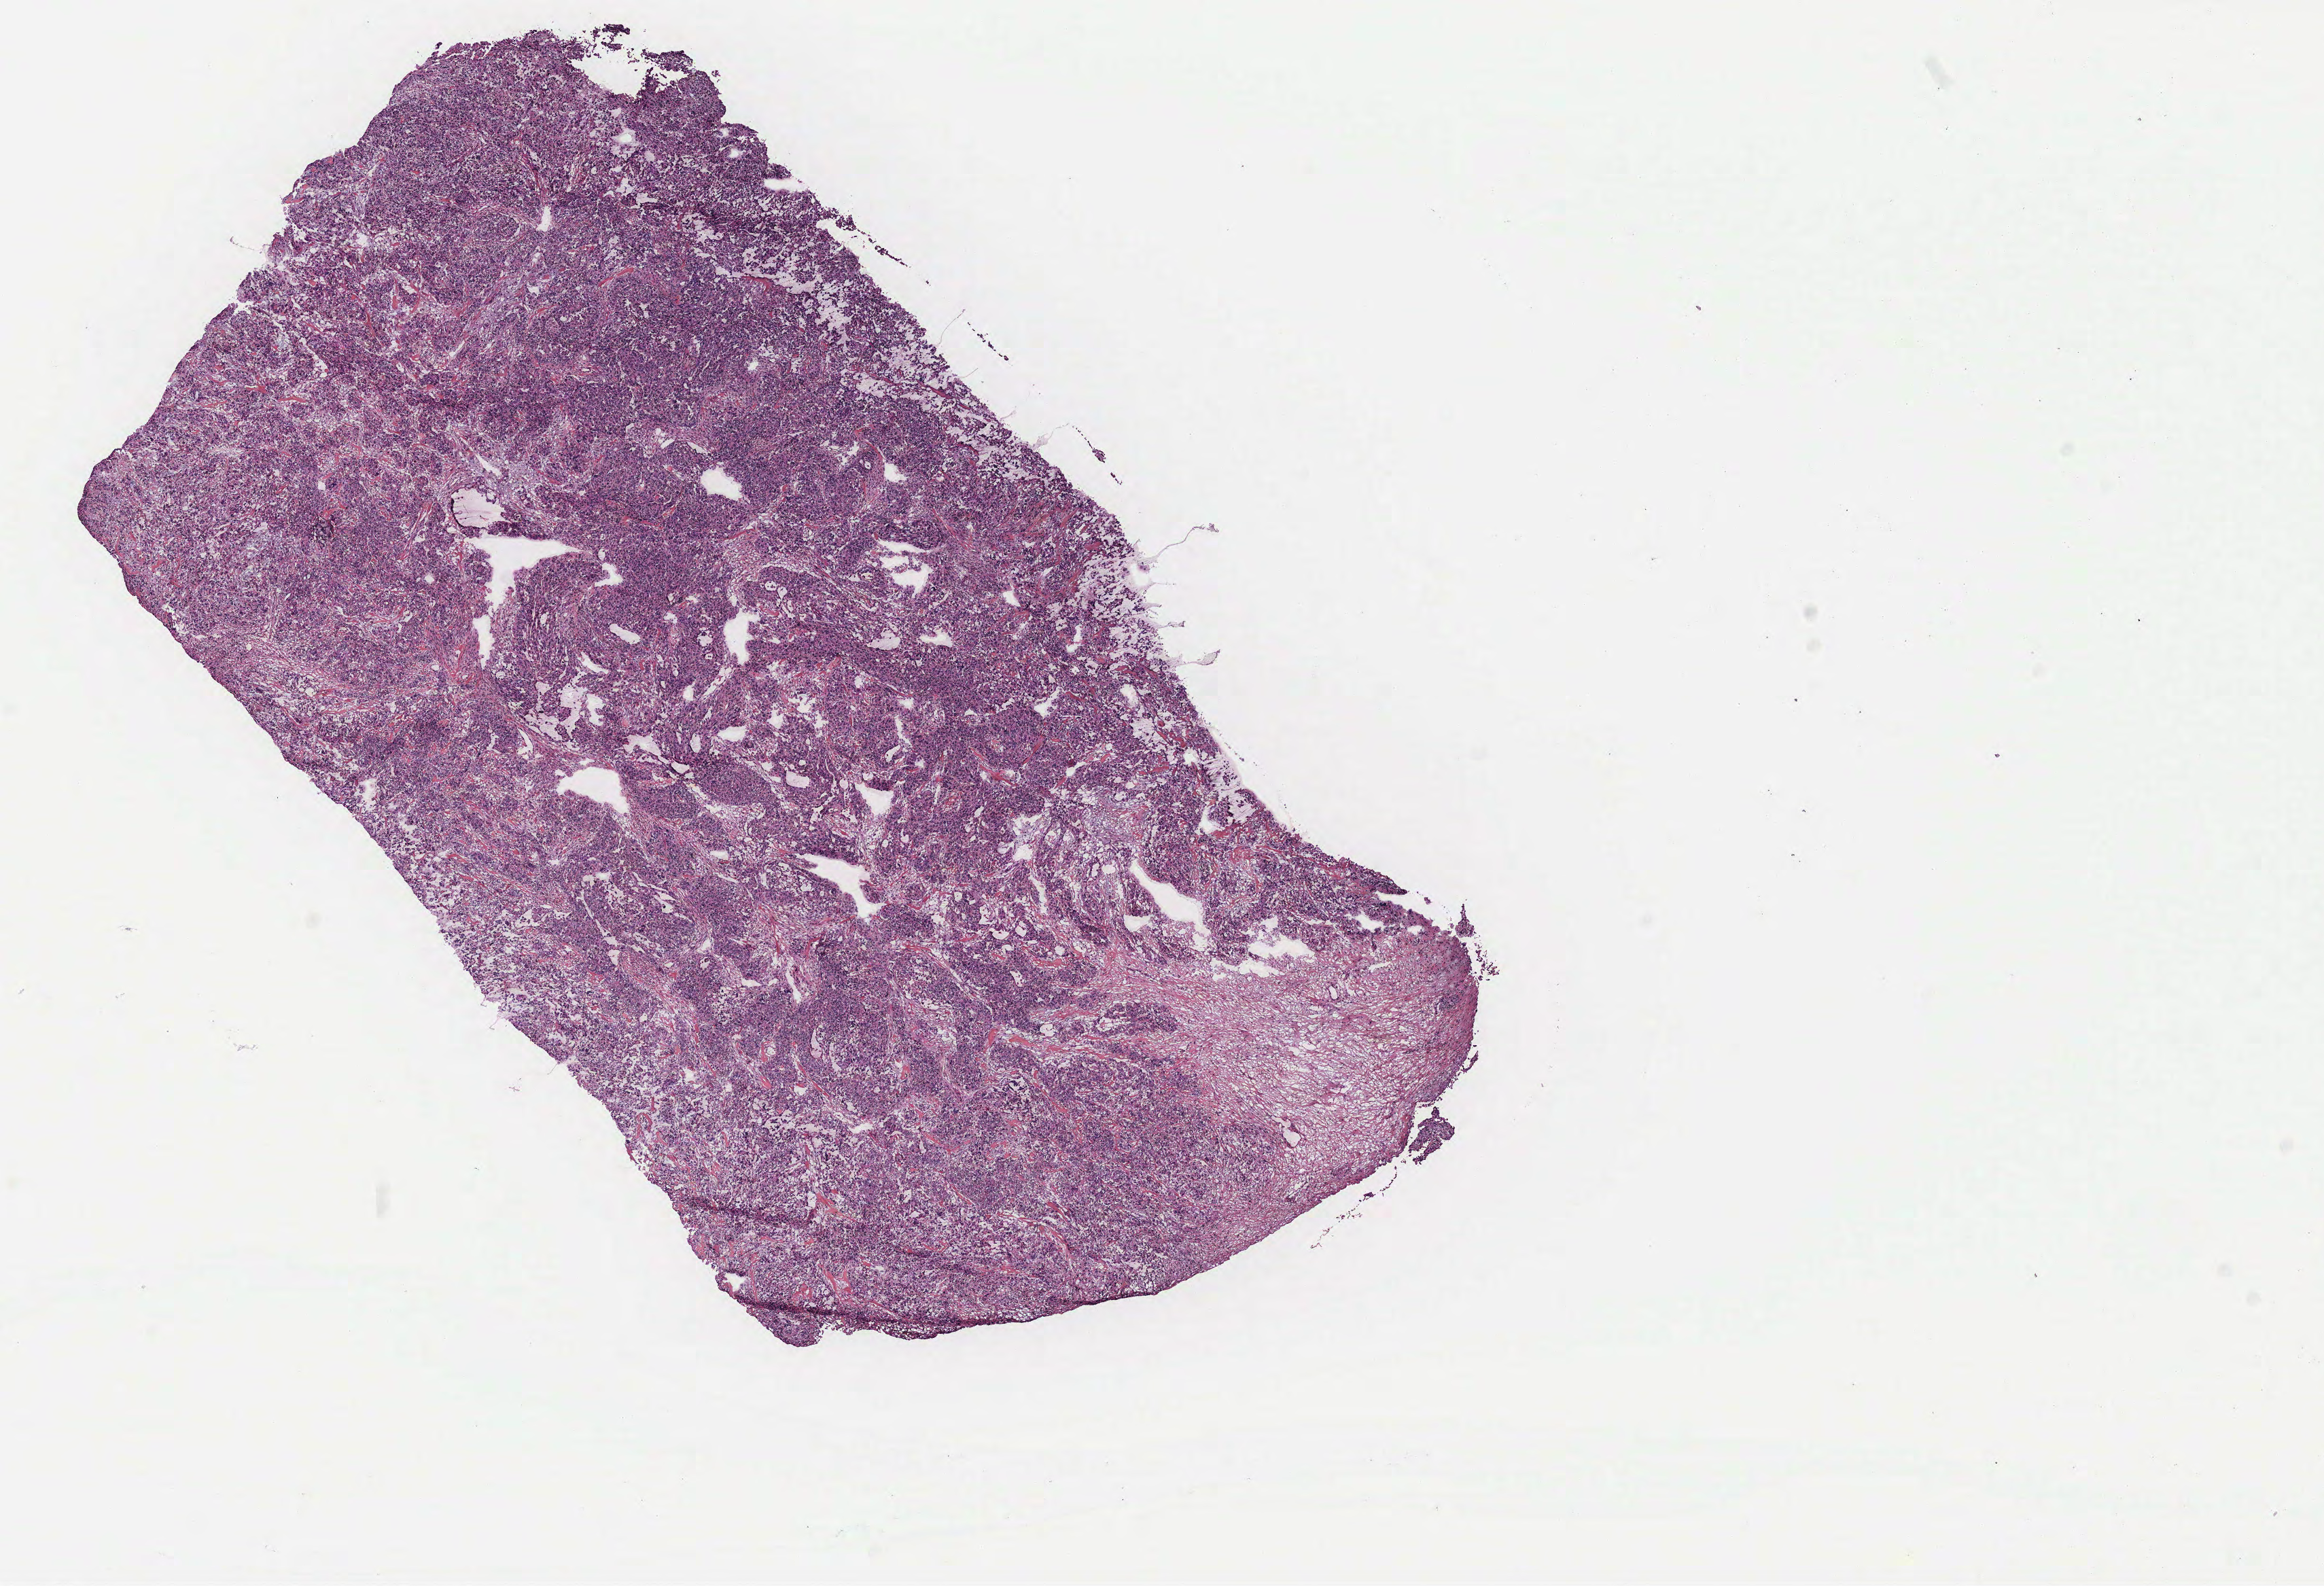
Whole-slide histology image, H&E — low-resolution overview of the scanned area, about 13.7 x 9.3 mm (acquisition: 40x scan); tumour tissue sample, ovary. Patient: female, age 50 years.
Primary tumour site (as recorded): ovary. Histologic diagnosis: Serous adenocarcinoma, NOS.